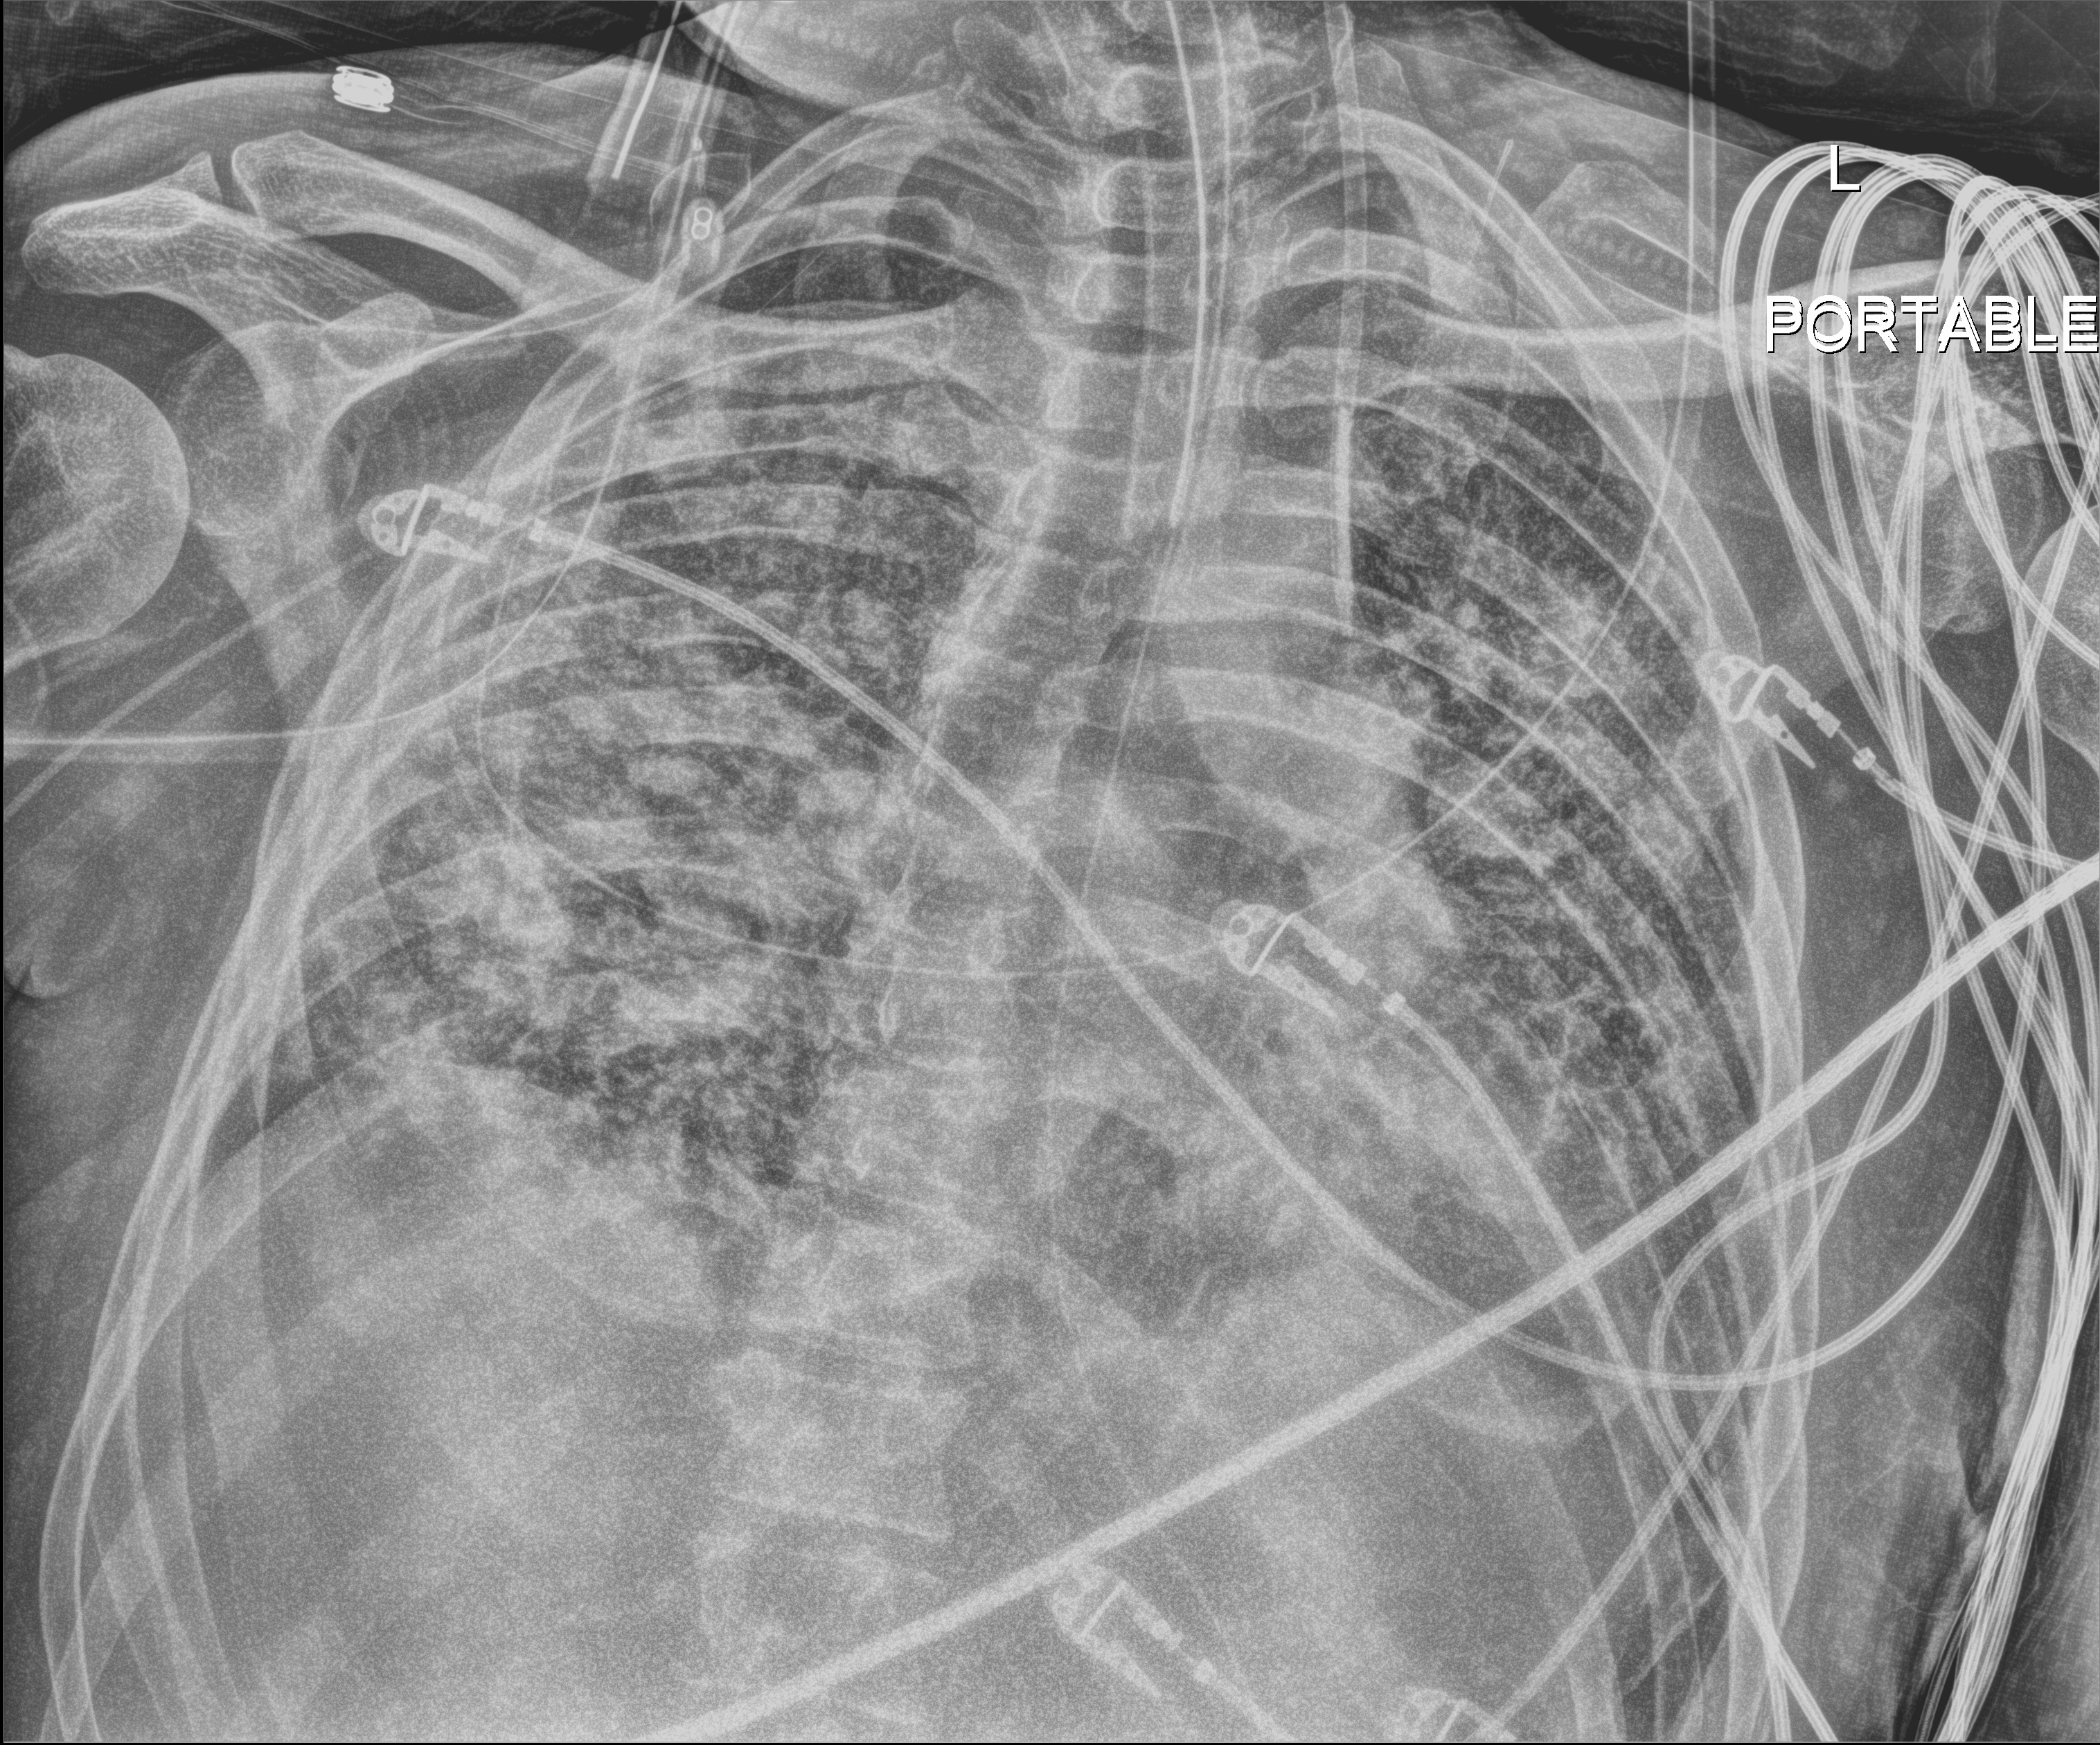
Portable chest radiograph; anteroposterior (AP) projection. Patient hospitalised with COVID-19; male, aged 18–59 years.
Hospital-stay facts (about this admission, not read from this image; timing relative to this image not recorded): length of hospital stay: 75 days.